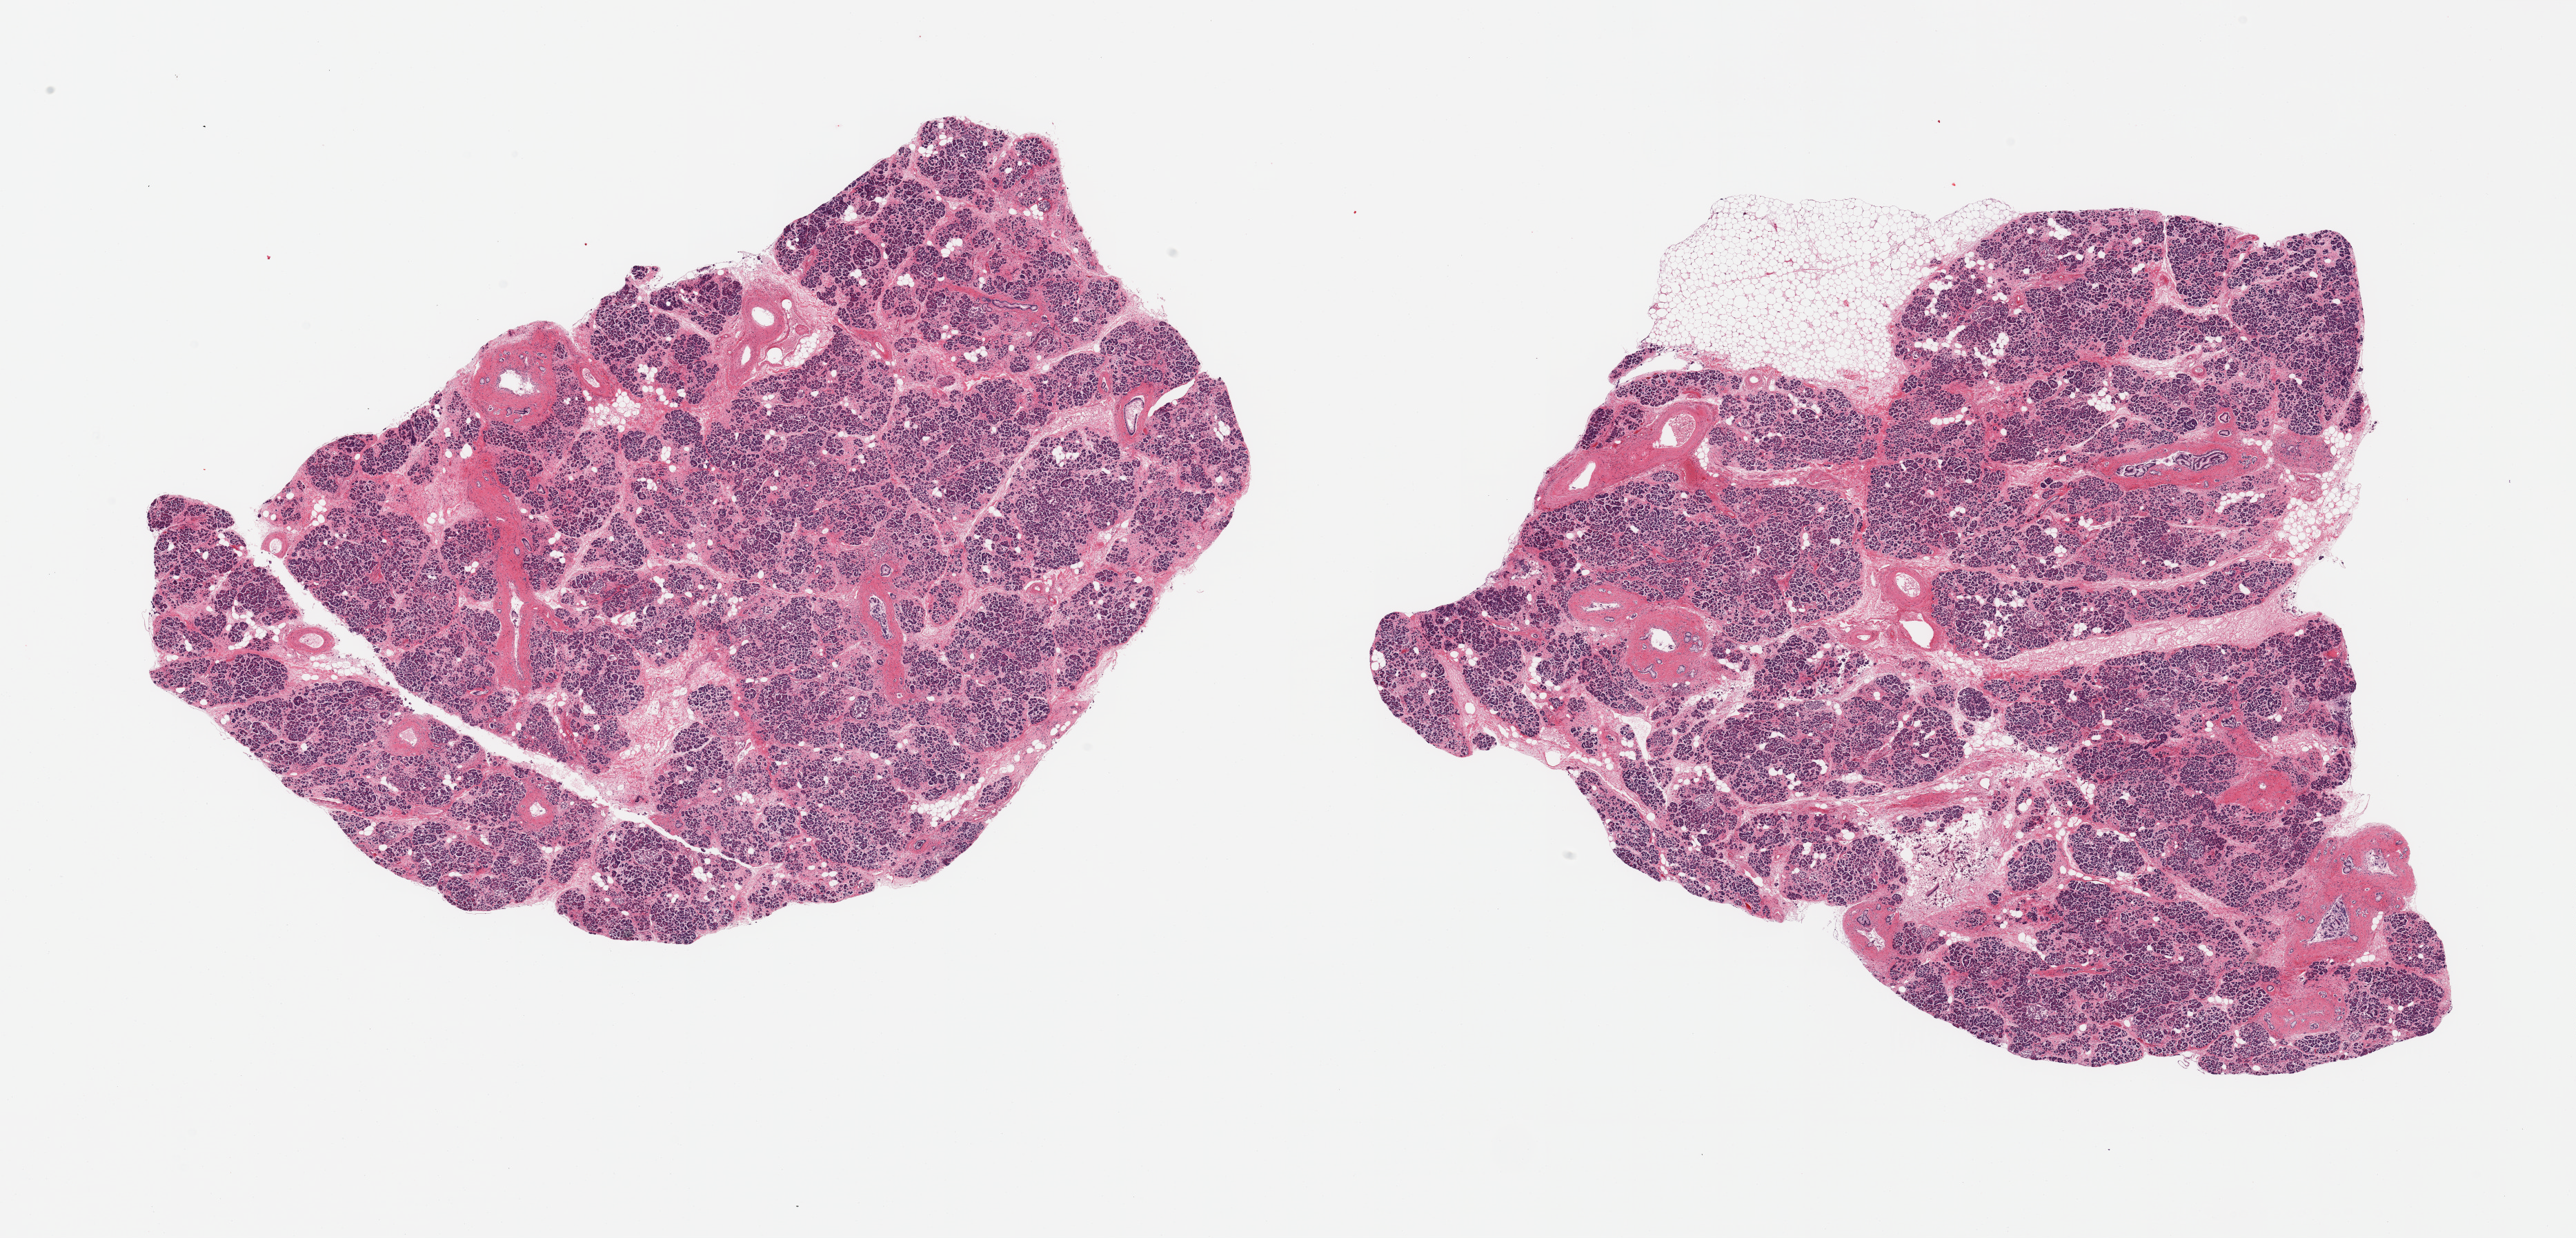
Digitized H&E-stained section — low-resolution overview of the scanned area, about 29.5 x 14.2 mm (slide scanned at 20x), PAXgene-fixed, paraffin-embedded tissue, target tissue: pancreas, donor tissue sample. Donor sex: female.
Review note (as recorded): 2 pieces; moderate interstitial fibrosis; 10% external fat on 1 piece.